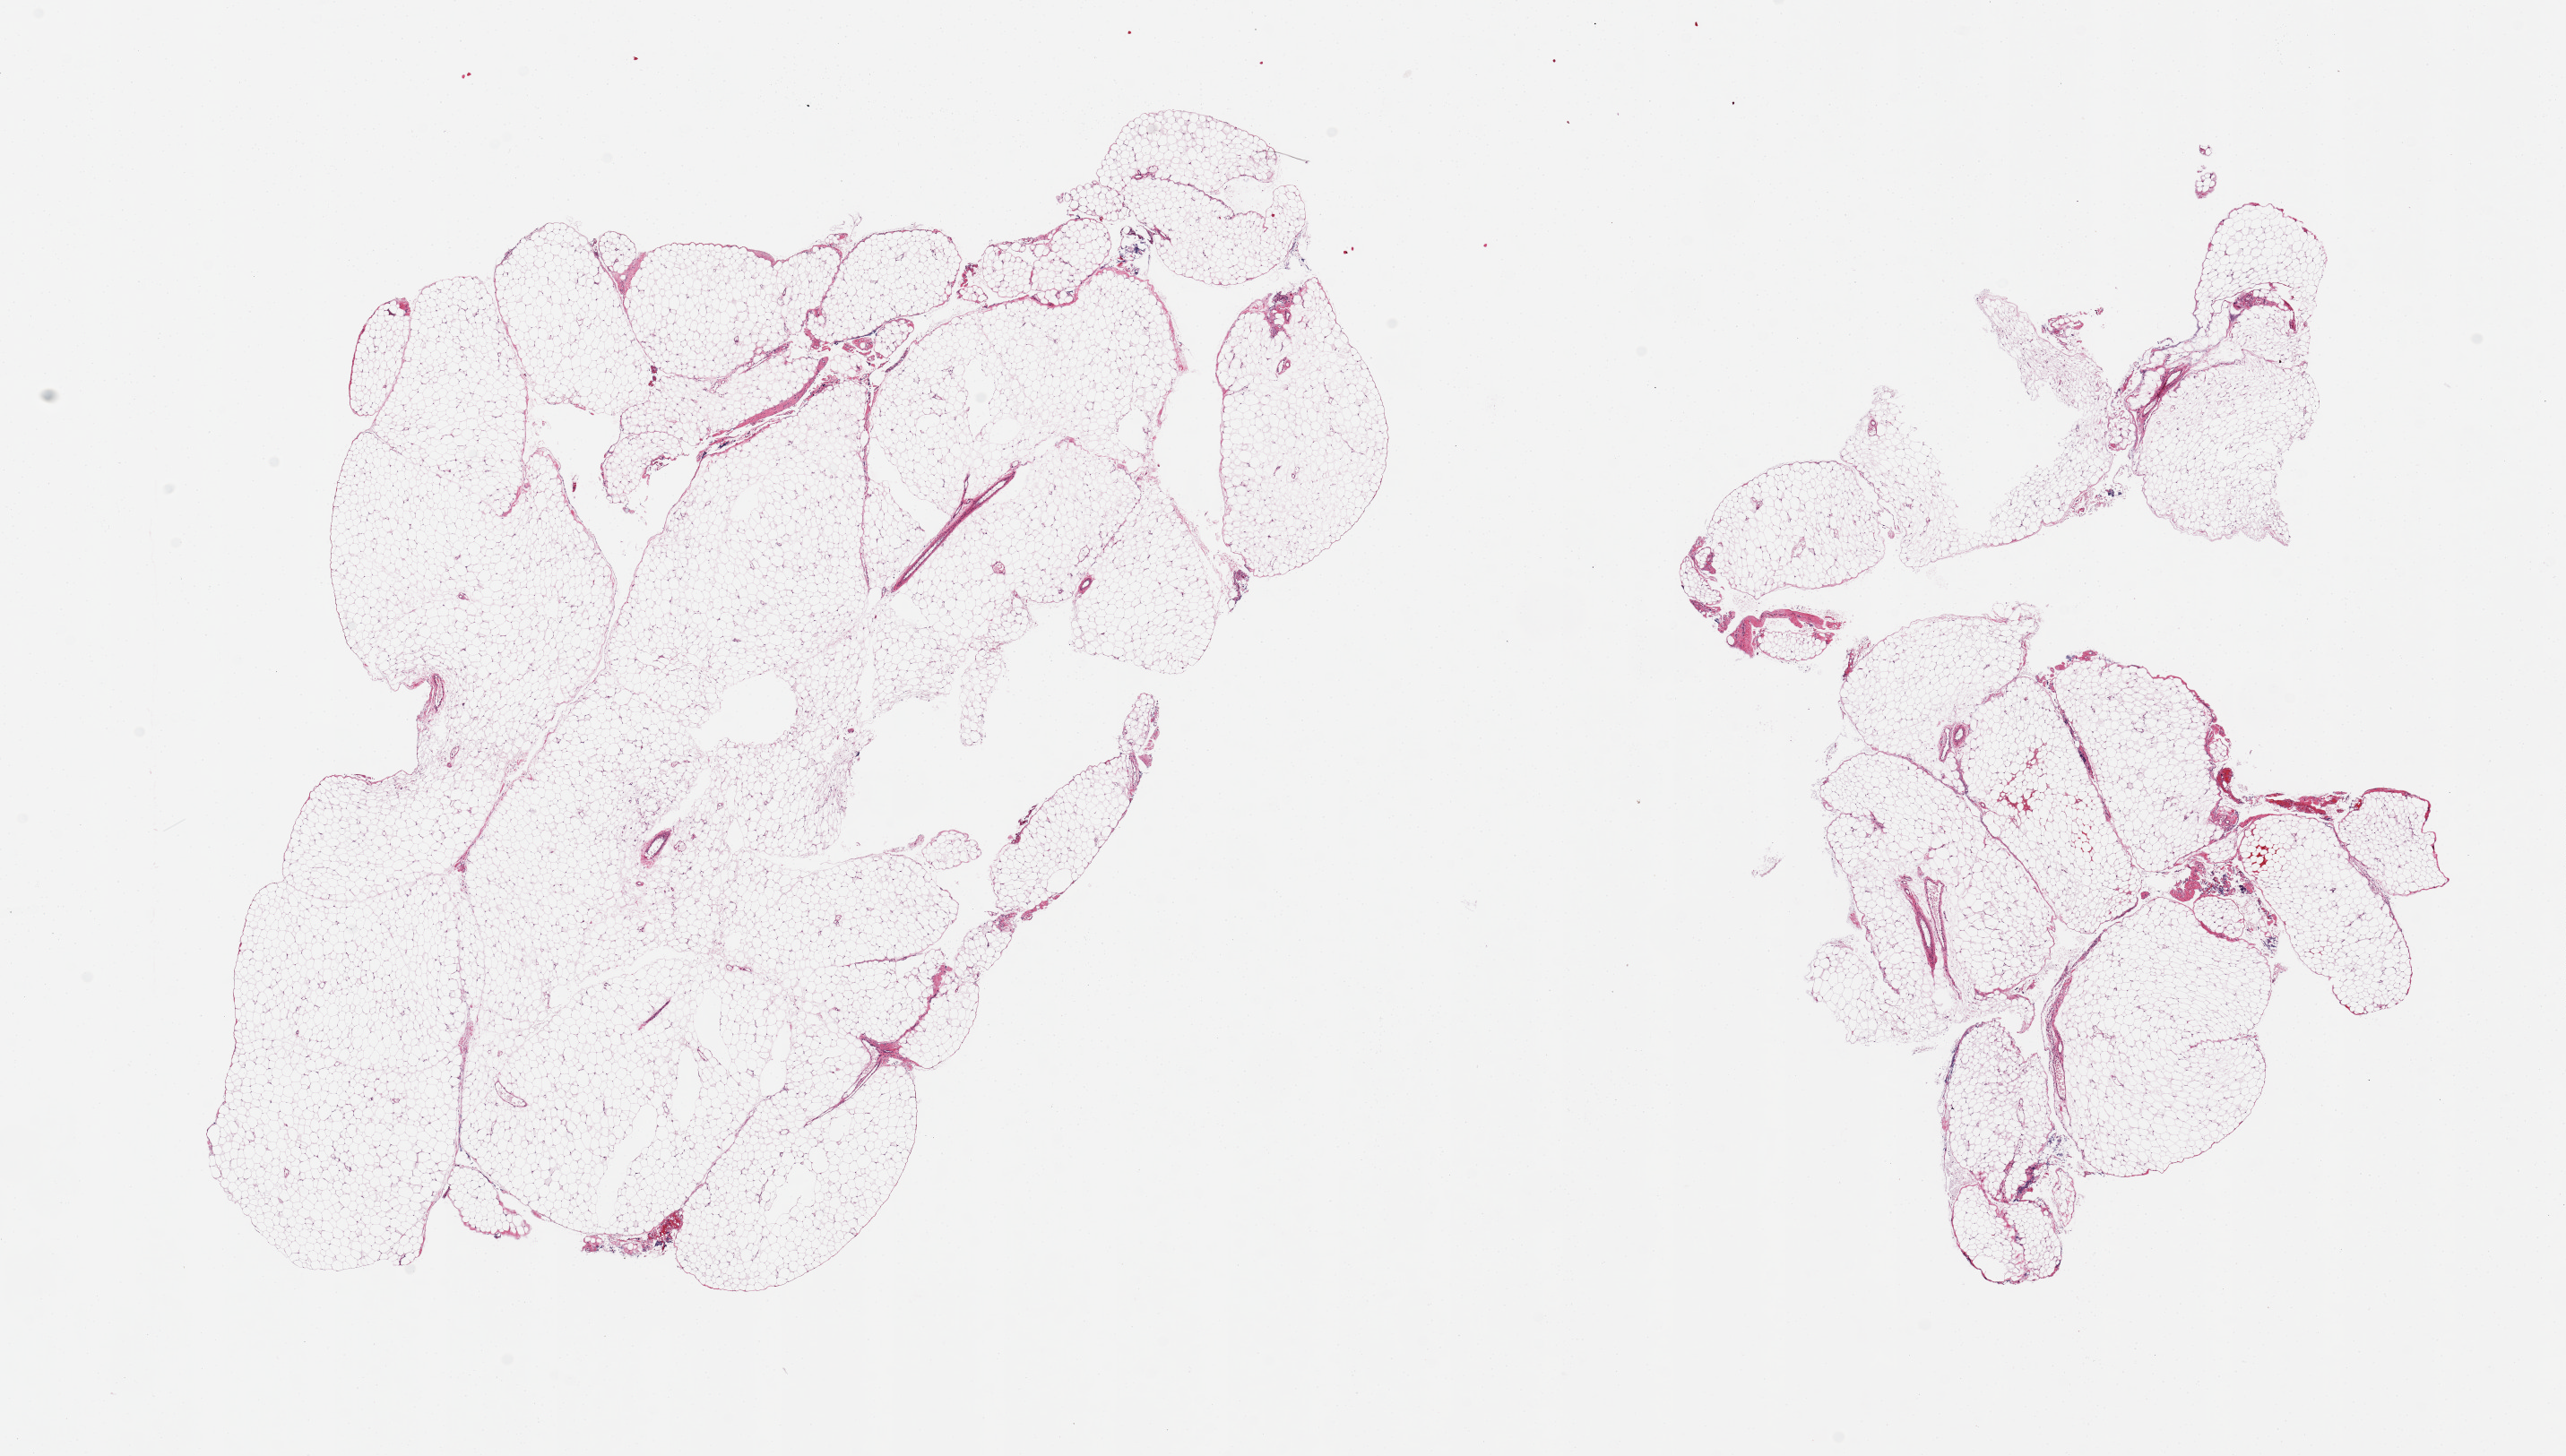
Digitized haematoxylin and eosin-stained section, brightfield, shown as a low-resolution overview of the whole scanned area (about 22.6 x 12.9 mm); PAXgene-fixed, paraffin-embedded tissue; target tissue: omentum; donor tissue sample. Male donor.
* reviewer comment on this tissue sample: 2 pieces; mature fat